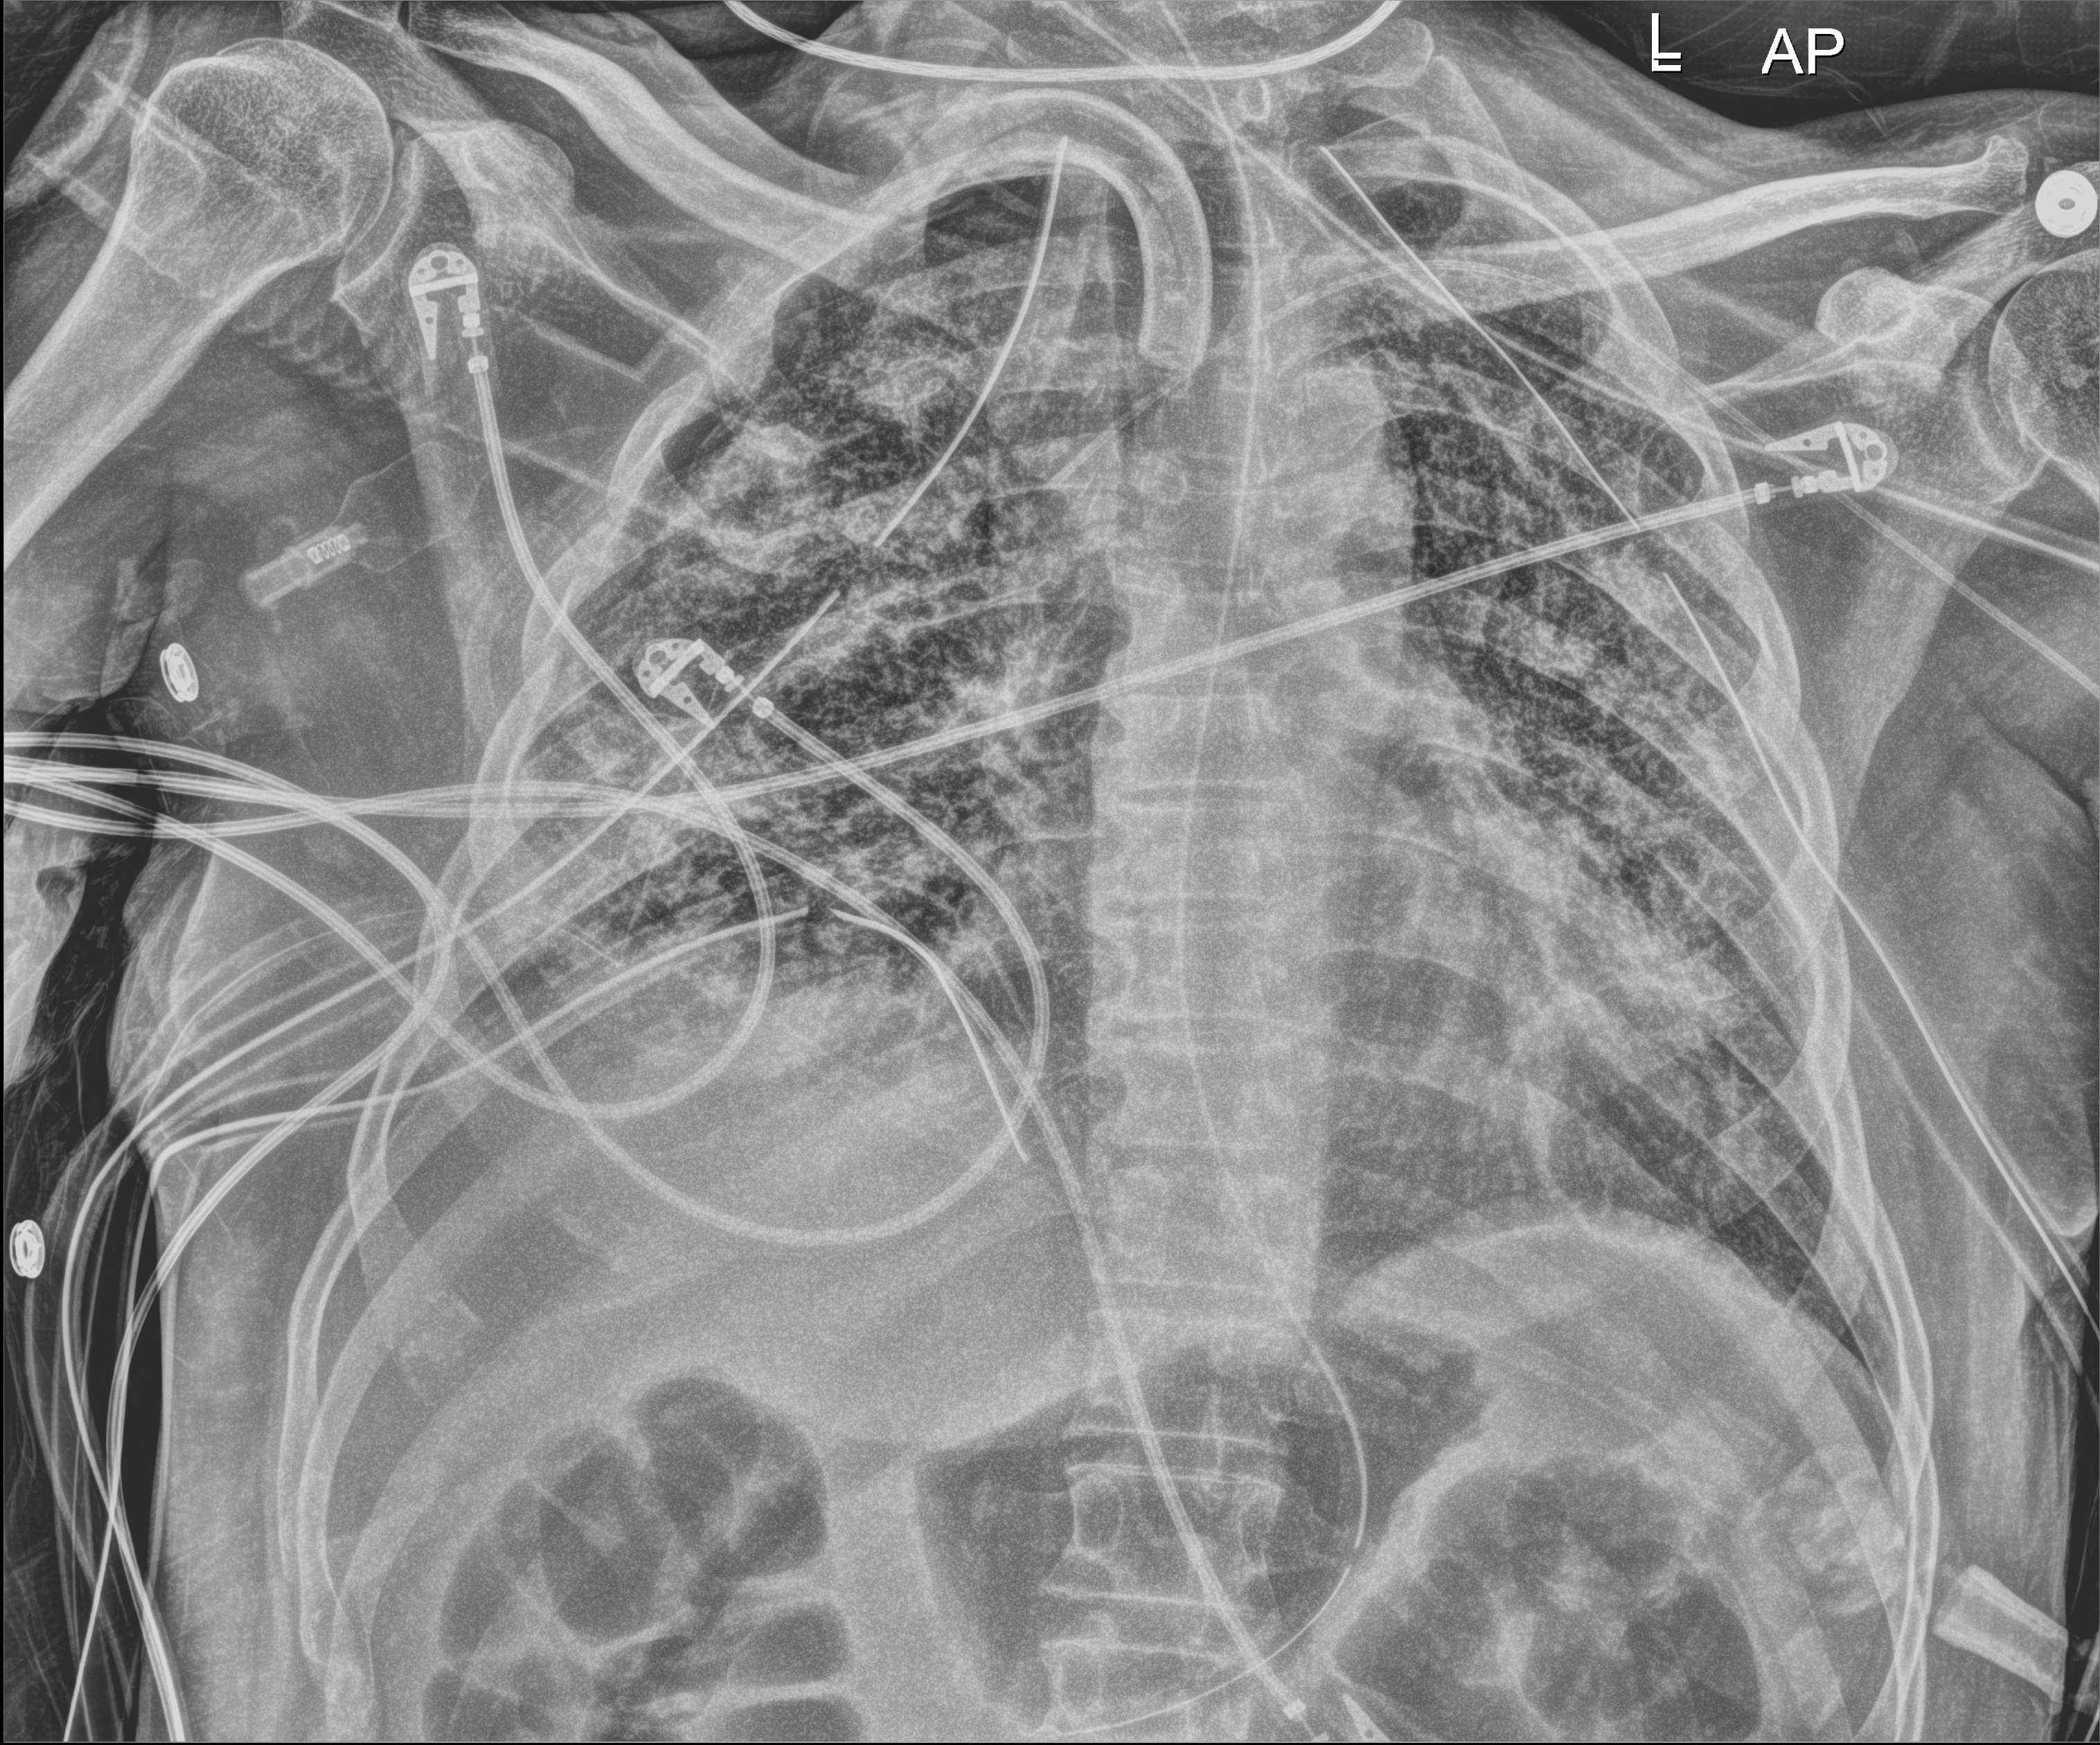
Bedside chest radiograph (digital radiography); anteroposterior (AP) projection. Male patient hospitalised with COVID-19, age 18–59 years.
Admission-level facts for this patient (not findings on this image; timing relative to this image not recorded):
- admitted to intensive care during this hospital stay: yes